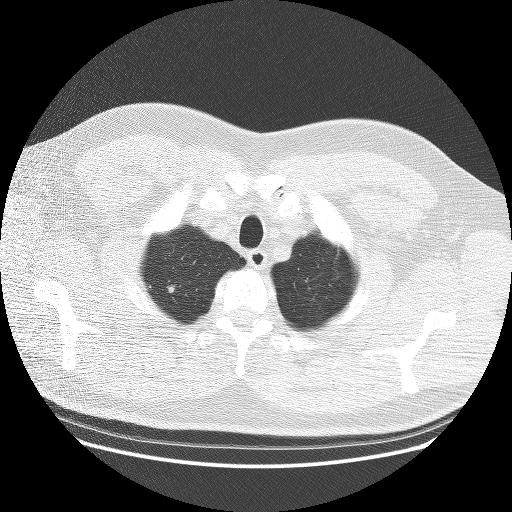
Axial slice from a low-dose chest CT screening exam. First (baseline) screen. Lung window (W 1500 / L -600 HU). 120 kVp. Slice 12 of 111 in the series. Male participant, aged 65 years at enrolment. Former smoker at enrolment.
• Expert reader's lesion annotation, bounding box <151,274,190,307> (left, top, right, bottom; pixels).
• Reader record for this screening exam (exam-level; its link to the box is not recorded): non-calcified nodule or mass ≥4 mm, right upper lobe, 11 × 9 mm, poorly defined margins, soft tissue attenuation.
• Lung cancer was diagnosed 44 days after this screen: adenocarcinoma, NOS, right upper lobe, moderately differentiated (G2), stage IA (AJCC 6th edition), 11 mm at pathology.